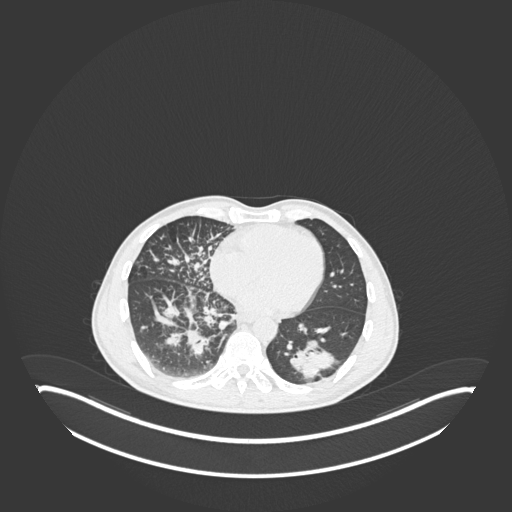
Chest CT, one axial slice. Slice 84 of 237 in the series (ordered by position). Reconstruction kernel B30f. Lung window (W 1500 / L -600 HU). 512 × 512 image matrix, field of view 500 × 500 mm. Patient: male, 49 years. From the clinical record (not read from this slice): clinical TNM (as recorded): T2b N1 M0.
Structures marked on this image (bounding box drawn by a radiologist):
- lung tumour (recorded histology: adenocarcinoma): bounding box (x1, y1, x2, y2) in pixels: (282, 339, 334, 381)